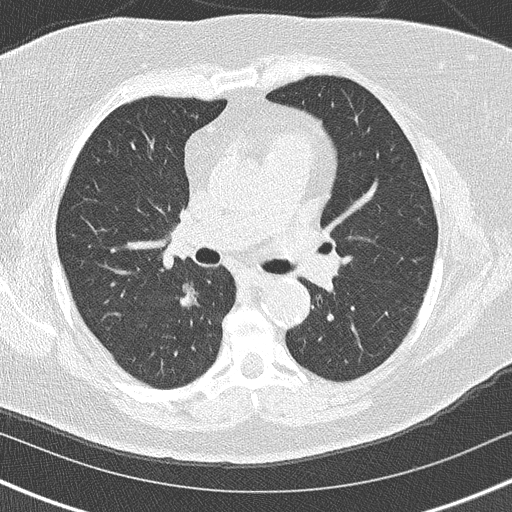
Axial slice from a low-dose chest CT screening exam. Second annual screen. Lung window (W 1500 / L -600 HU). 2 mm slice thickness. 120 kVp. Slice 60 of 152 in the series. 512 × 512 image matrix, field of view 320 × 320 mm. Female, age 60 years at enrolment.
- Expert-annotated lung lesion, bounding box <149,270,217,327> (left, top, right, bottom; pixels).
- The exam's reader record, not a measurement of the box and not confirmed to be the same lesion: non-calcified nodule or mass ≥4 mm, right lower lobe, 20 × 19 mm, soft tissue attenuation, pre-existing on the prior screen: yes; interval growth: yes.
- Official screen result: positive, other.
- Later outcome: lung cancer diagnosed 139 days after this screen — bronchiolo-alveolar carcinoma, non-mucinous, right lower lobe, stage IA (AJCC 6th edition), 15 mm at pathology.